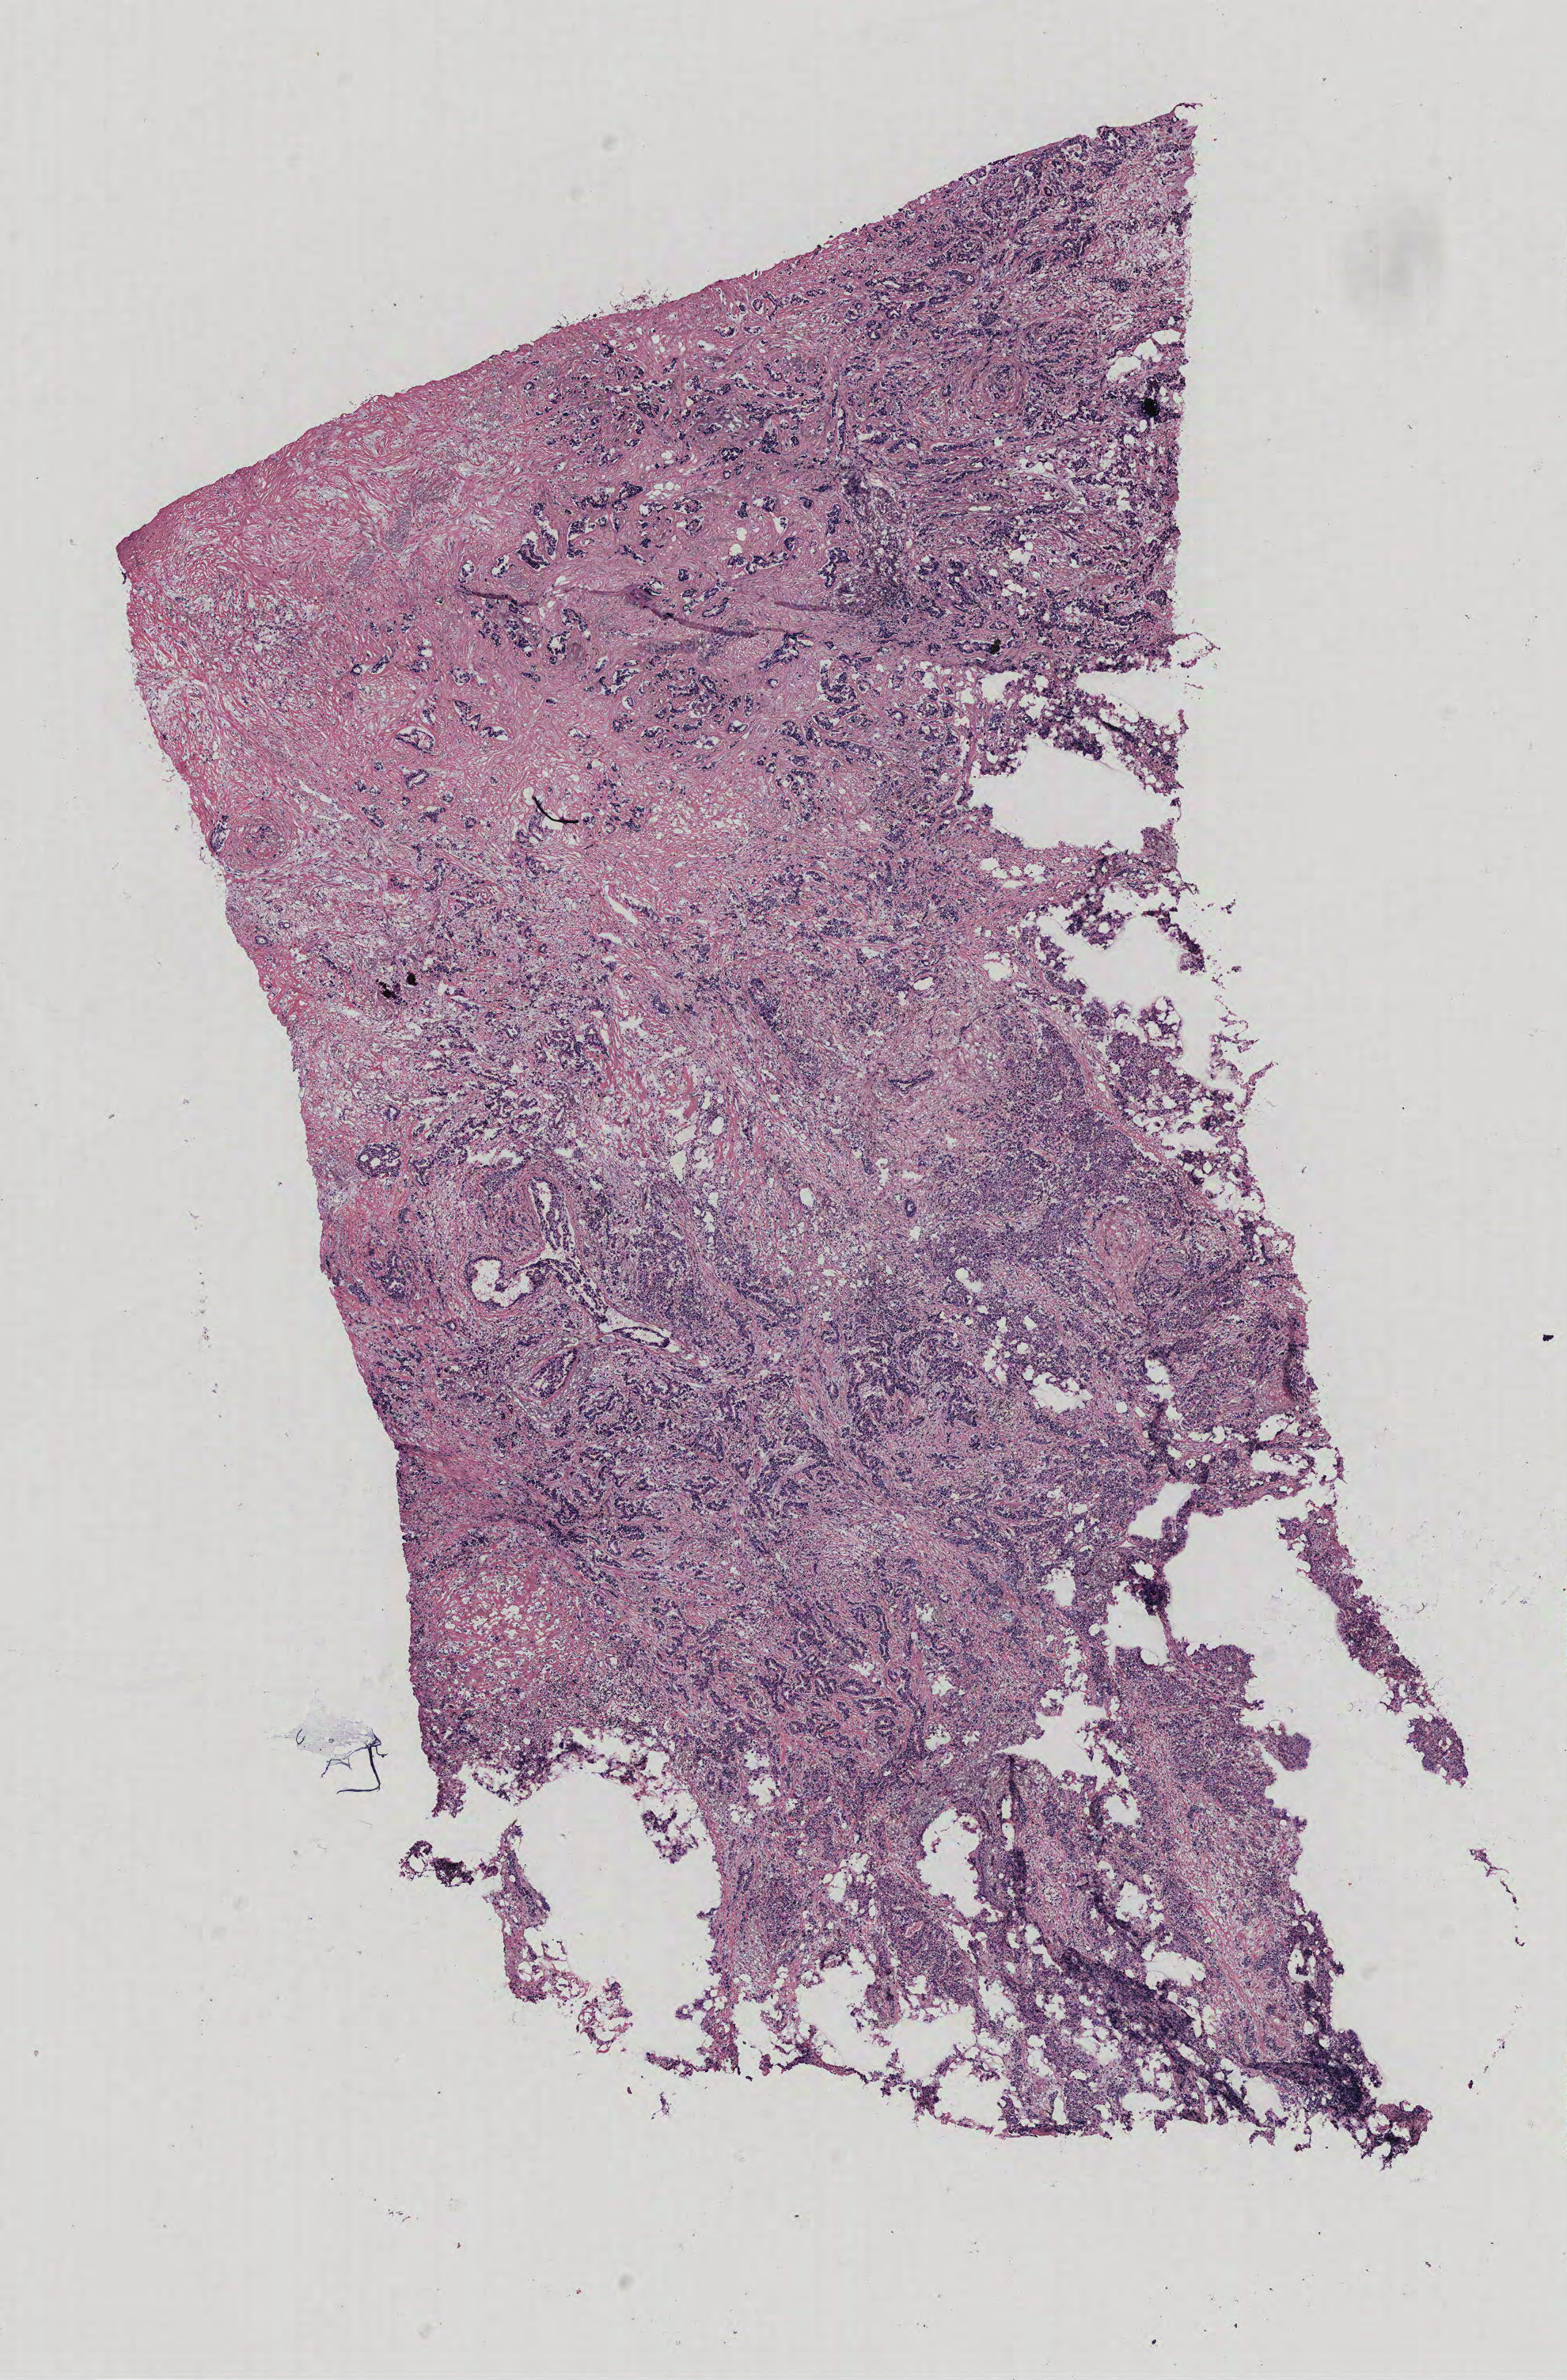
Digitized H&E-stained tissue section (whole slide) — a low-resolution overview of the entire scanned area, about 7.9 x 12.0 mm (slide scanned at 40x), breast, tumour tissue. 77-year-old female patient.
Diagnosis: Infiltrating duct carcinoma, NOS. AJCC pathologic stage: IIIA.